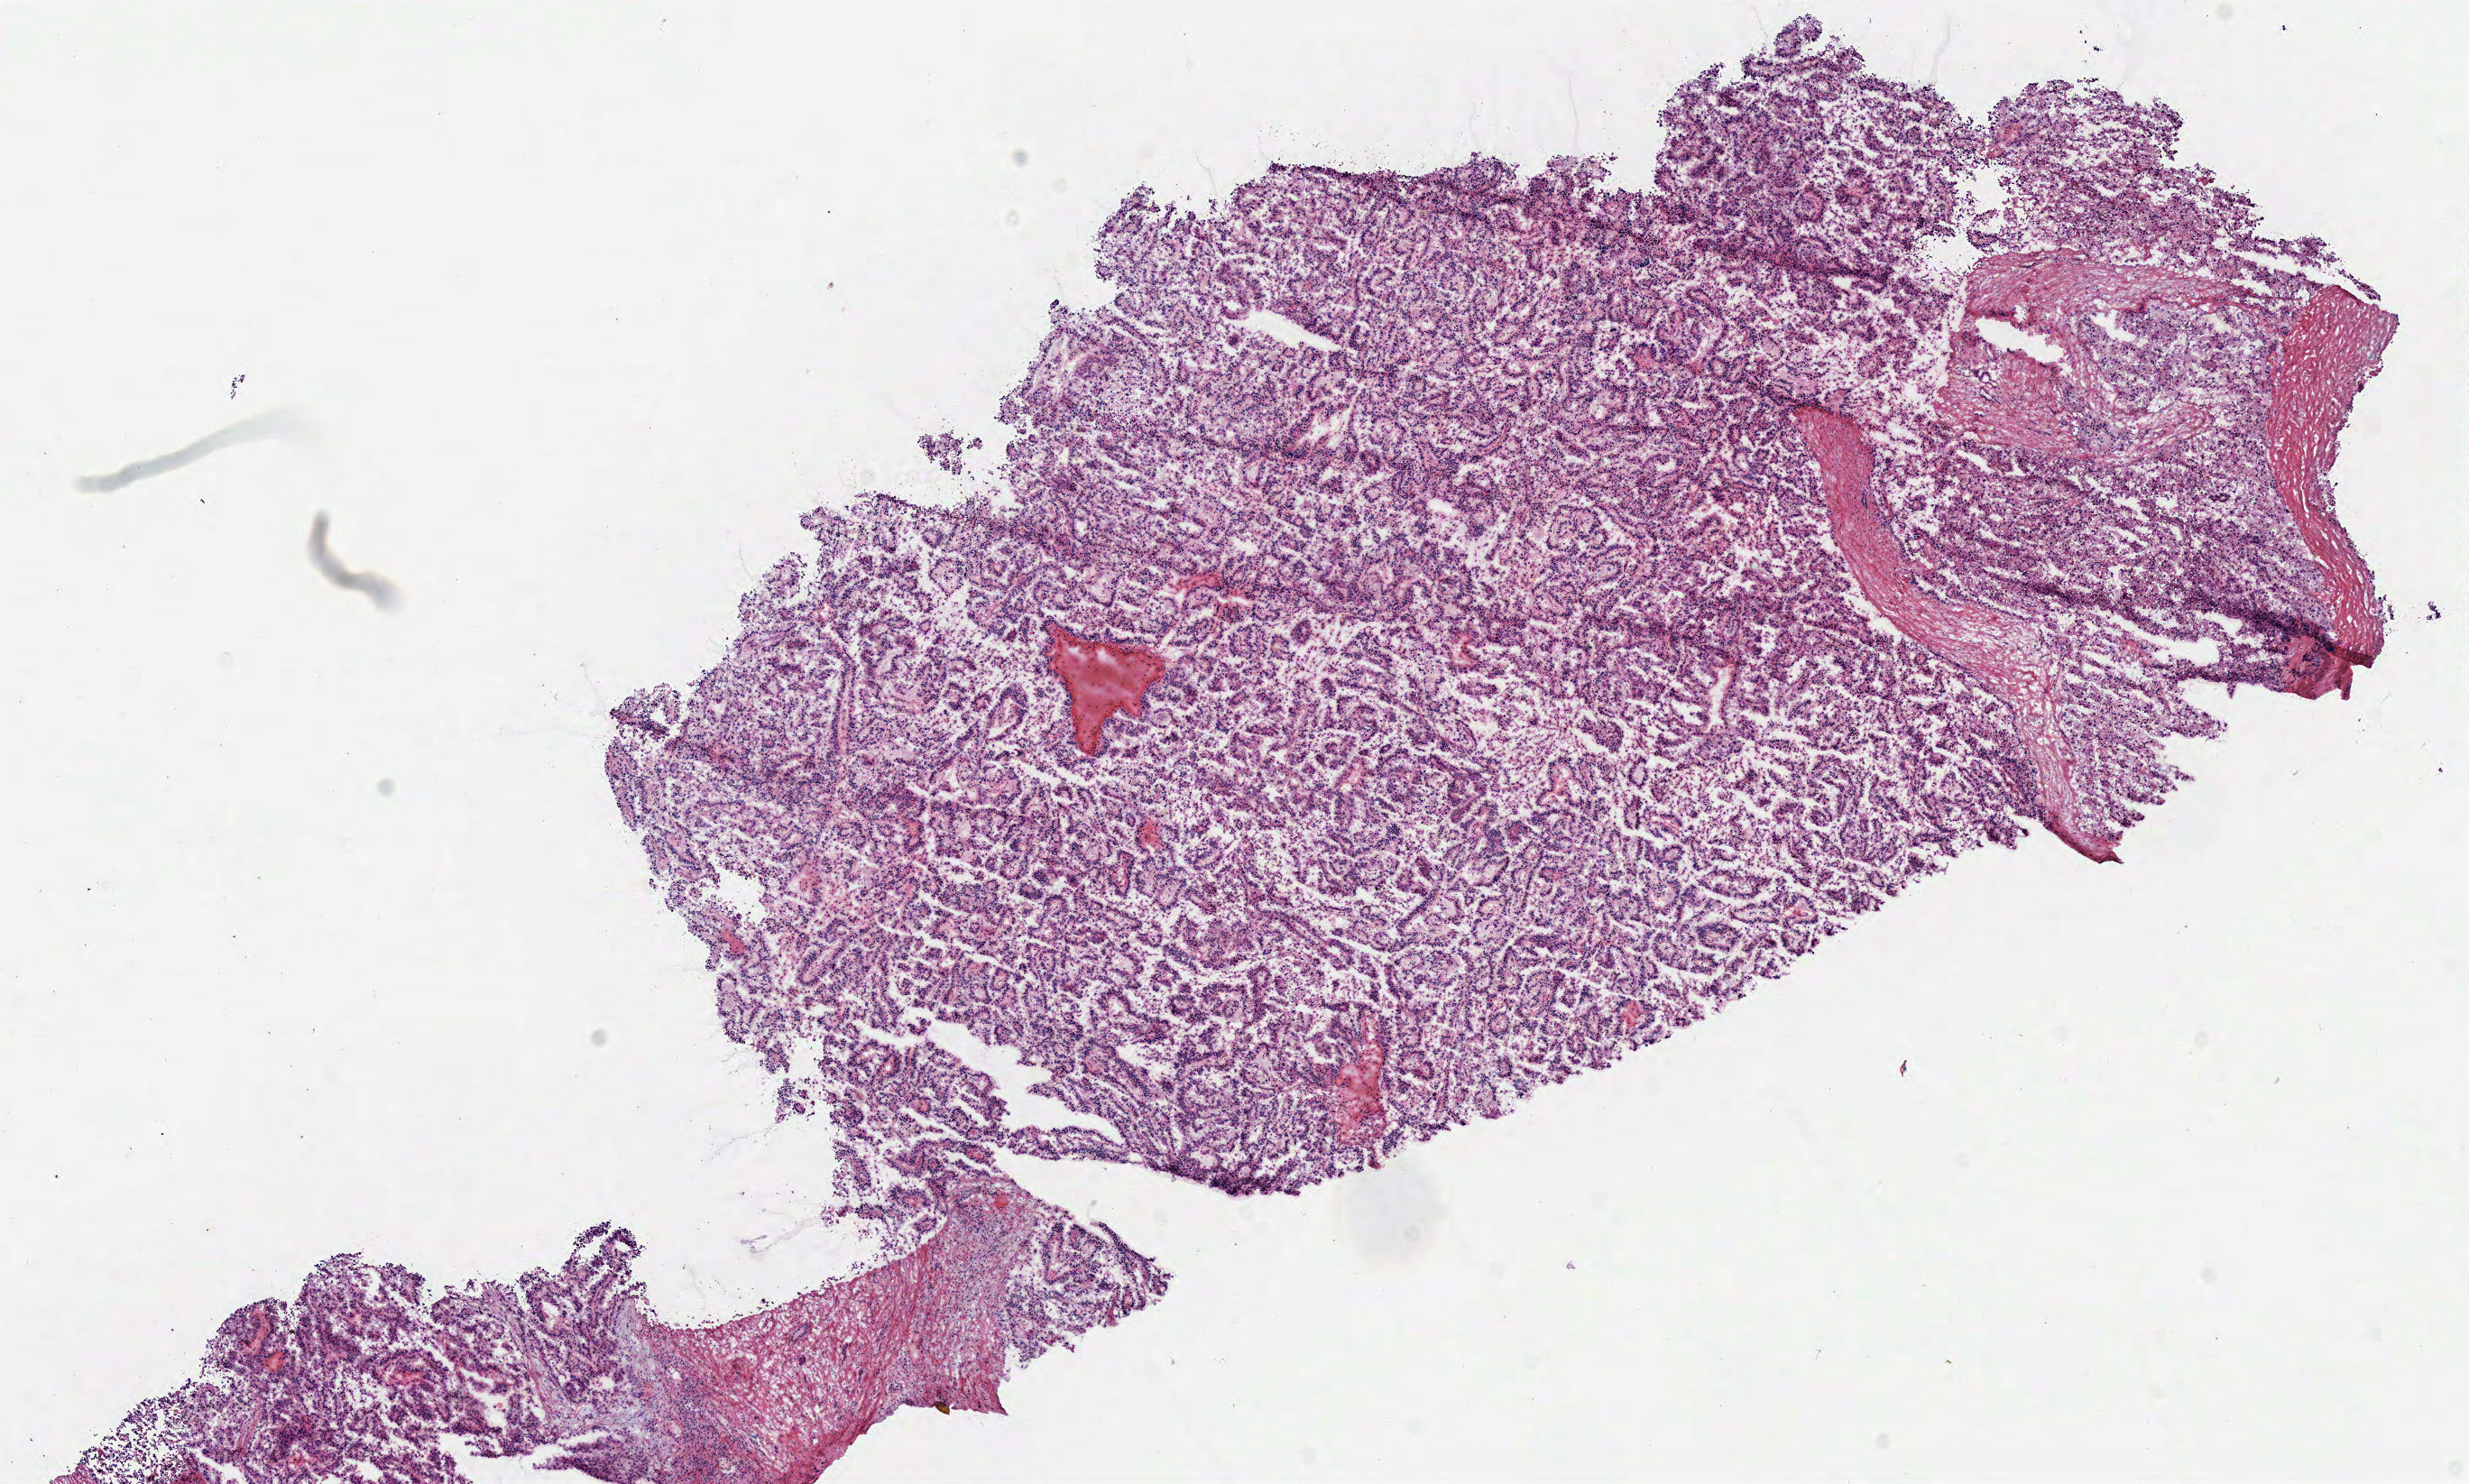
Whole-slide histology image, H&E-stained — a low-resolution overview of the entire scanned area, about 10.8 x 6.5 mm (from a 40x scan). Frozen section from the top of the tissue portion. Kidney, primary tumour sample. Male patient; age at initial diagnosis 31 years. Pathologist review of this section (percent, as recorded): tumour cells 90%, tumour nuclei 80%, normal cells 0%, stromal cells 10%, necrosis 0%.
• laterality: right
• diagnosis: Papillary adenocarcinoma, NOS
• AJCC pathologic stage: III